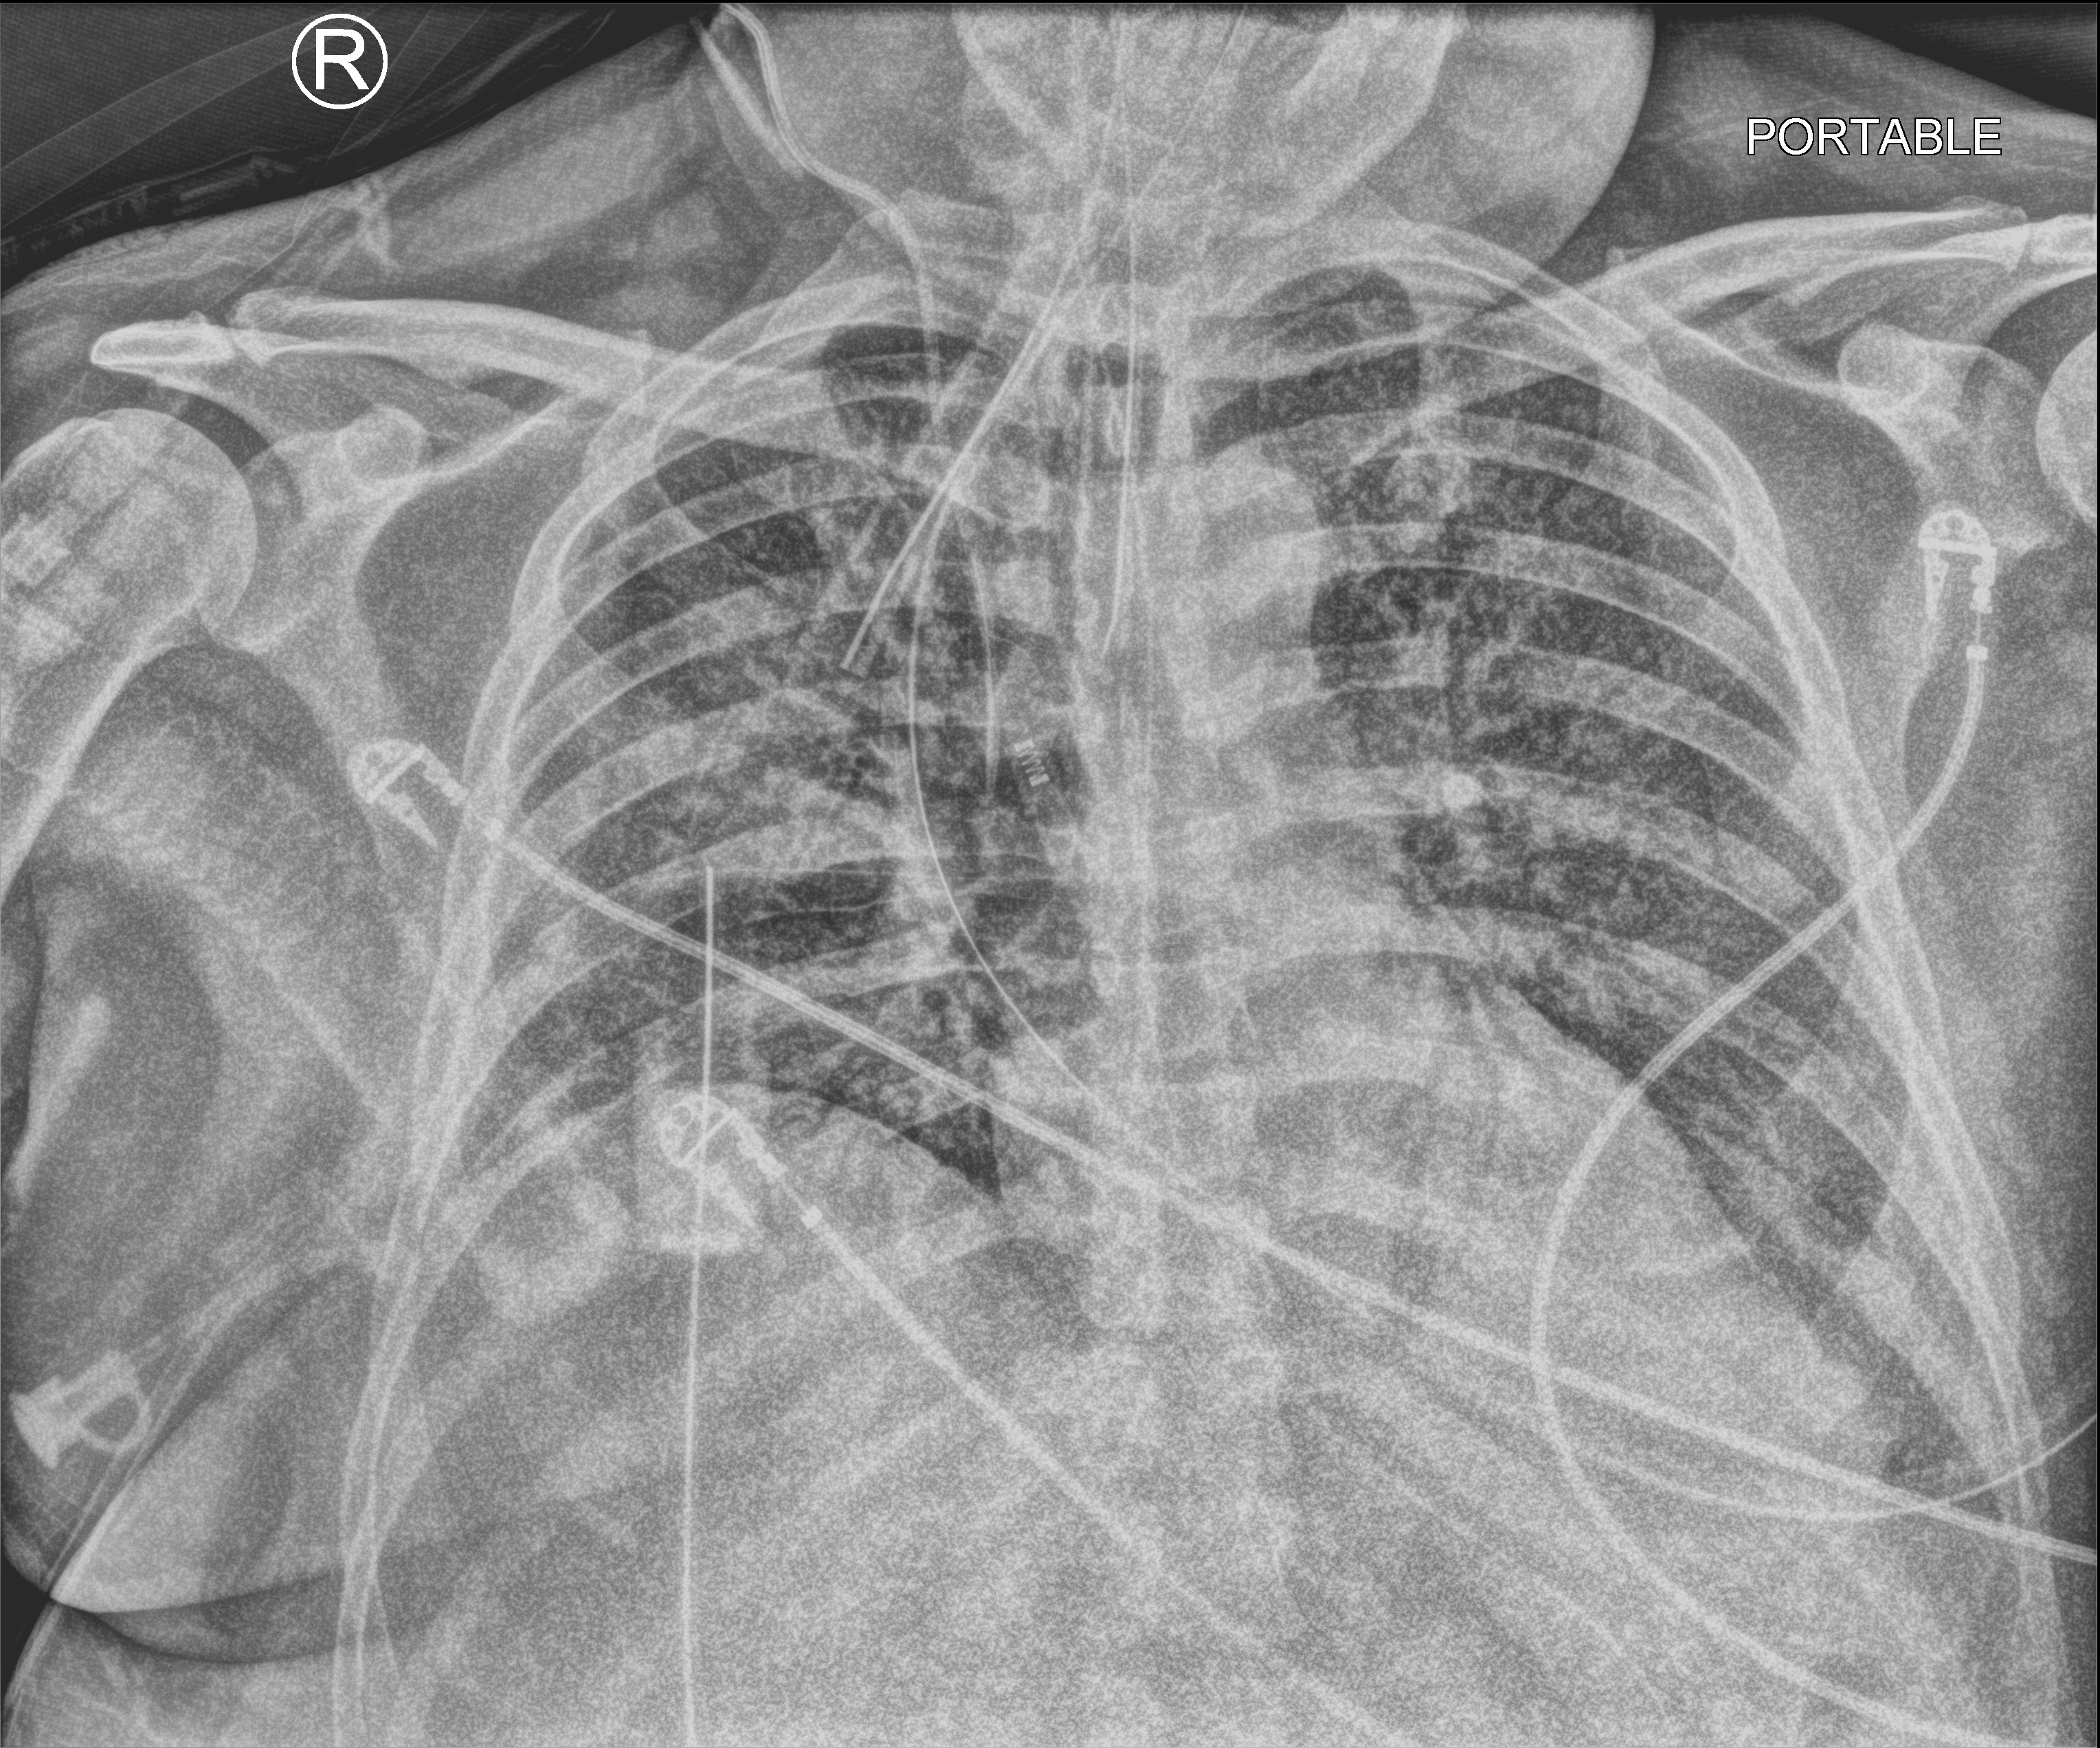
Bedside chest radiograph (computed radiography); anteroposterior (AP) projection. Male patient hospitalised with COVID-19, age 18–59 years.
Hospital-stay facts (about this admission, not read from this image; timing relative to this image not recorded): admitted to intensive care during this hospital stay: yes; chronic kidney disease (admission record): no.